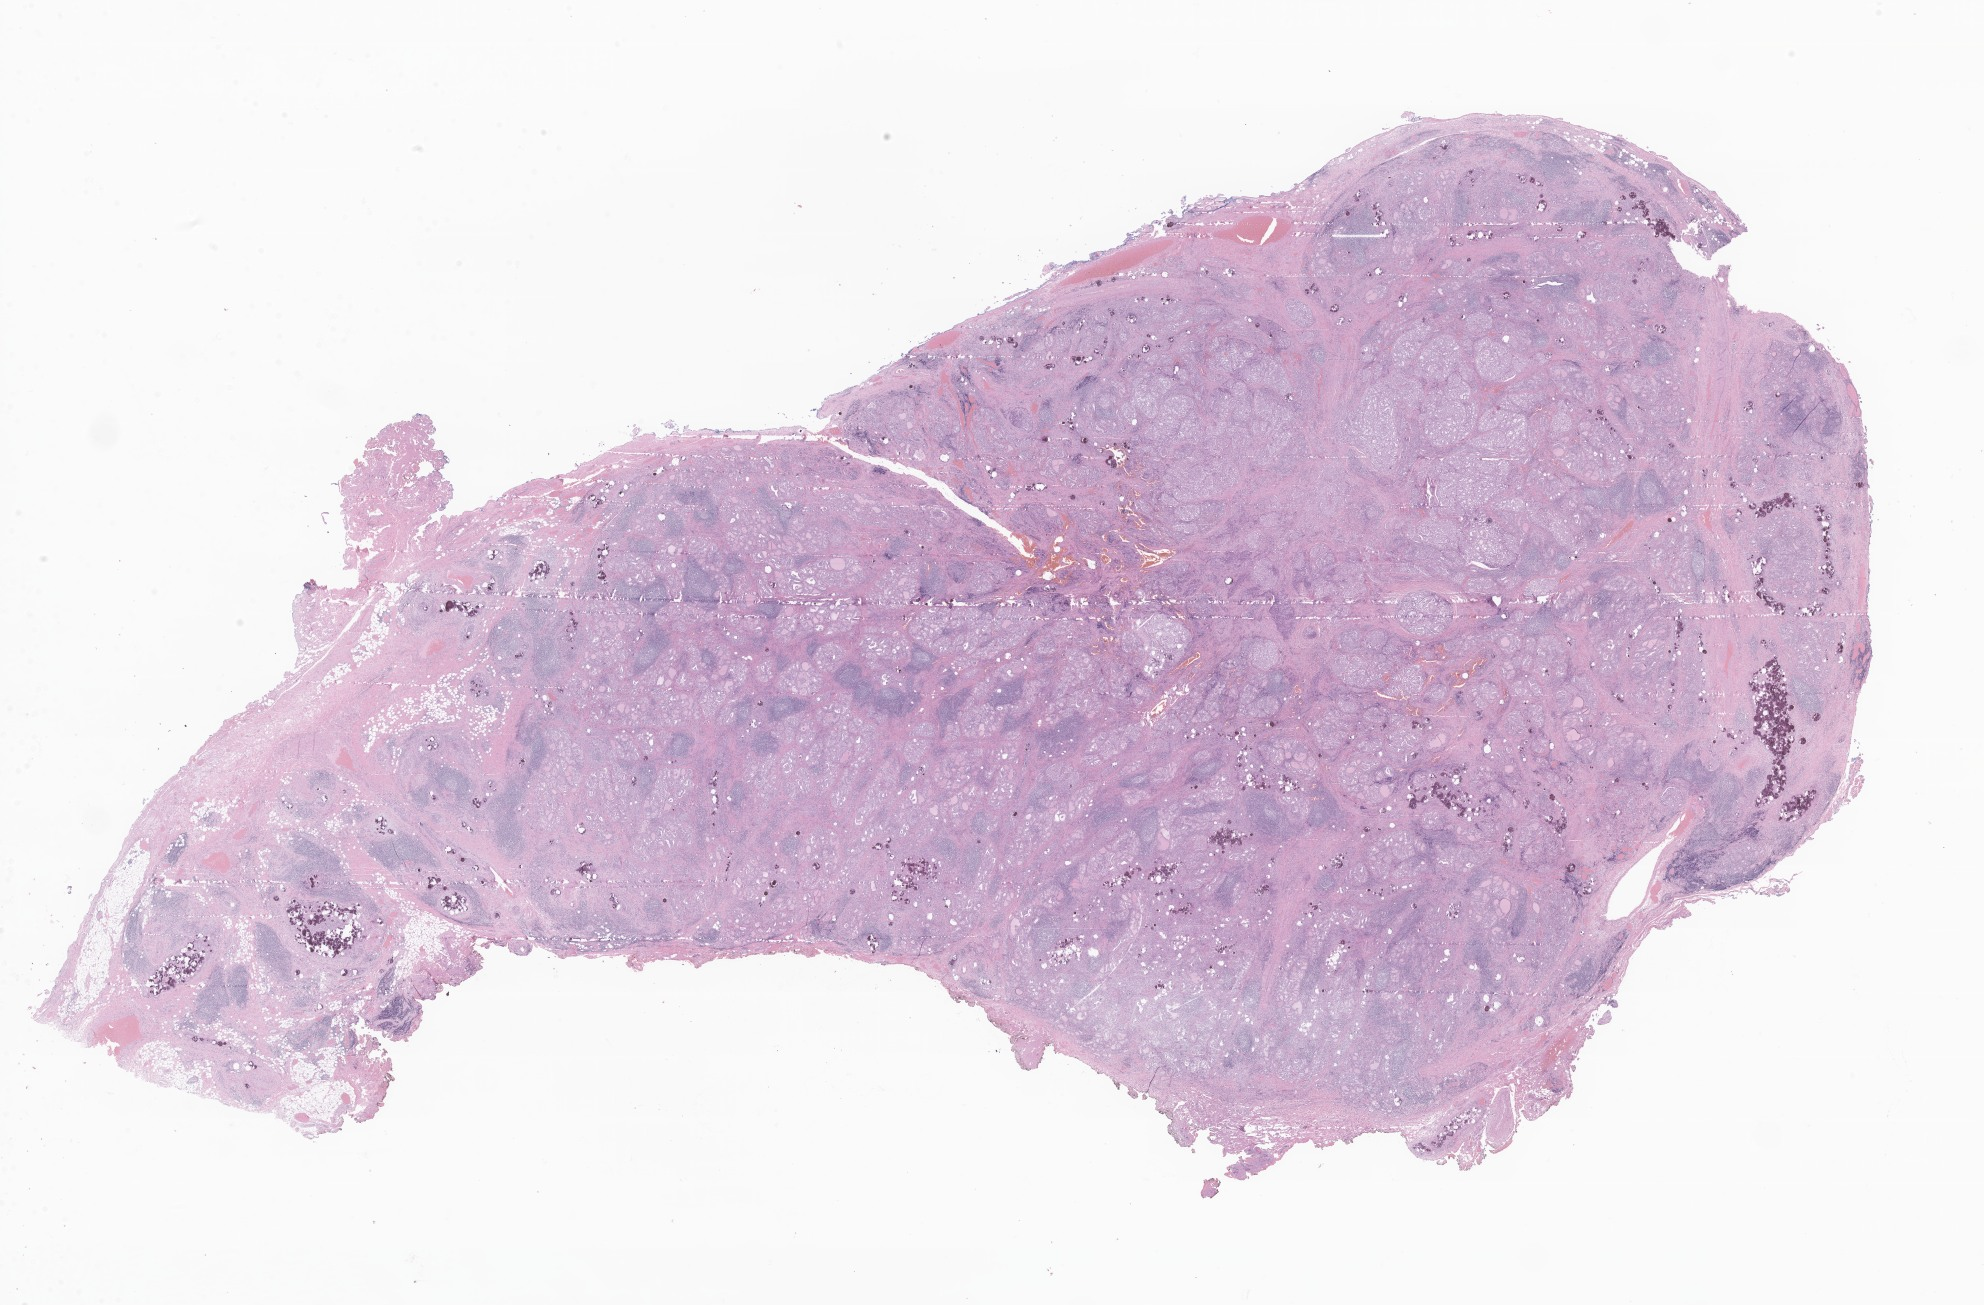
Whole-slide image, haematoxylin and eosin stain of tumor tissue from the thyroid — a low-resolution overview of the entire scanned area, about 33.5 x 22.0 mm. Formalin-fixed paraffin-embedded section. Female patient, age 168 months (14 years).
Recorded diagnosis: Neoplasm, uncertain whether benign or malignant.